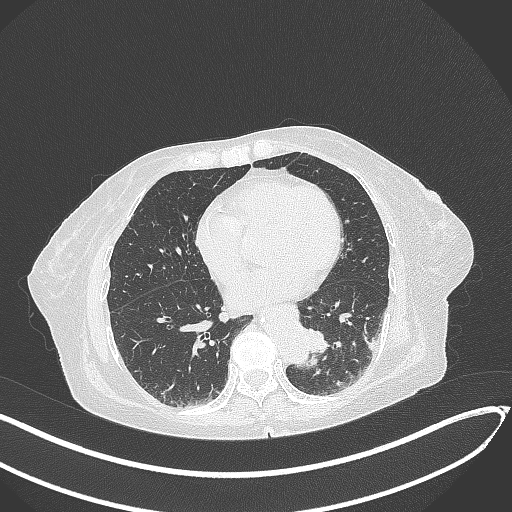
Chest CT, one axial slice; position 86 of 324 along the scan axis; lung window (W 1500 / L -600 HU); 1 mm slice thickness; 512 × 512 image matrix, field of view 400 × 400 mm. Female patient, age 82 years. Case-level facts recorded for this patient, not image findings: clinical TNM (as recorded): T1b N0 M1.
Annotated regions visible in this slice (rectangle marked by the reading radiologist):
- lung tumour (recorded histology: adenocarcinoma): box from (x=301, y=323) to (x=340, y=361) px